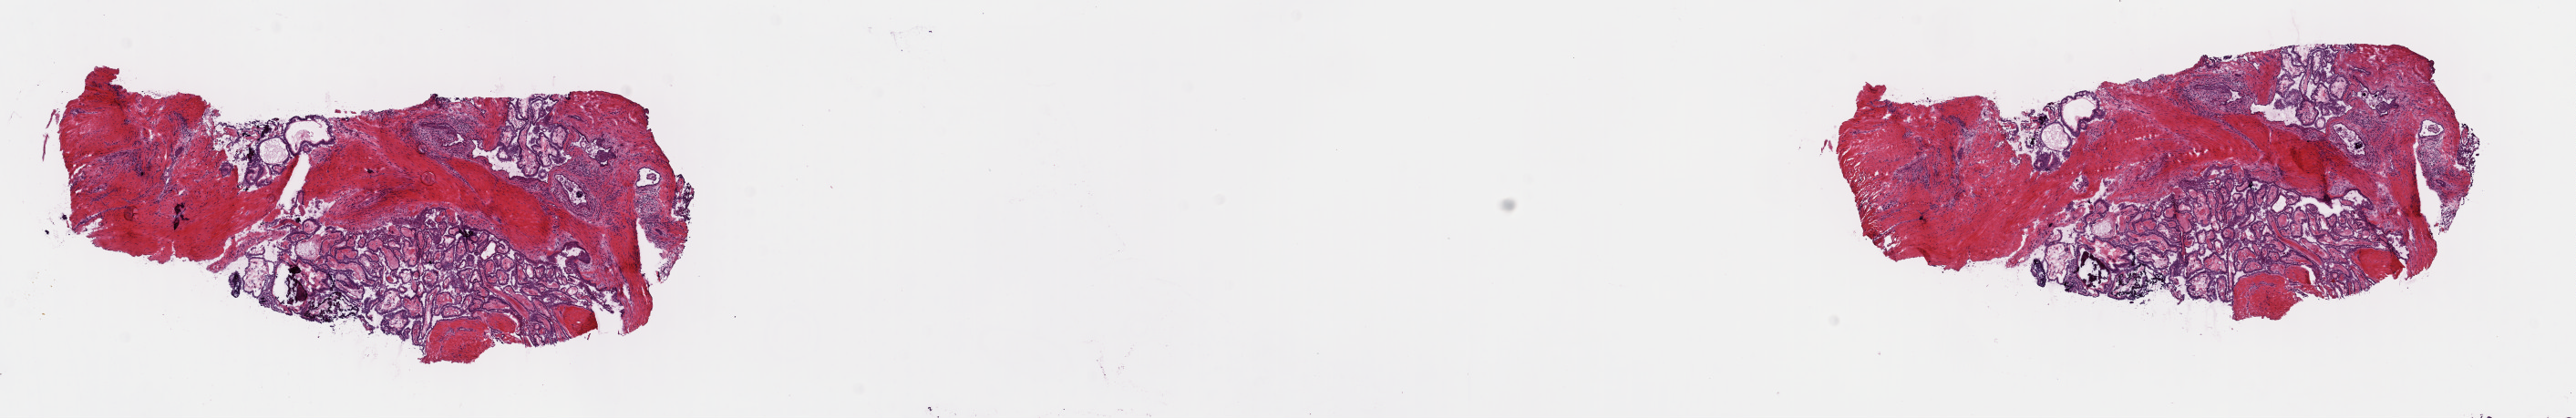
H&E-stained whole-slide image — a low-resolution overview of the entire scanned area, about 22.3 x 3.6 mm (acquisition: 40x scan). Frozen section. Thyroid, primary tumour sample. Patient: male, age at initial diagnosis 51 years. Slide review estimates, as recorded: tumour cells 65%, tumour nuclei 65%, normal cells 0%, stromal cells 35%, necrosis 0%. Infiltration values recorded for this section: lymphocyte infiltration 0%, monocyte infiltration 0%, neutrophil infiltration 0%.
AJCC pathologic stage: III (7th edition). Diagnosis: Papillary adenocarcinoma, NOS (thyroid gland). Laterality: midline.